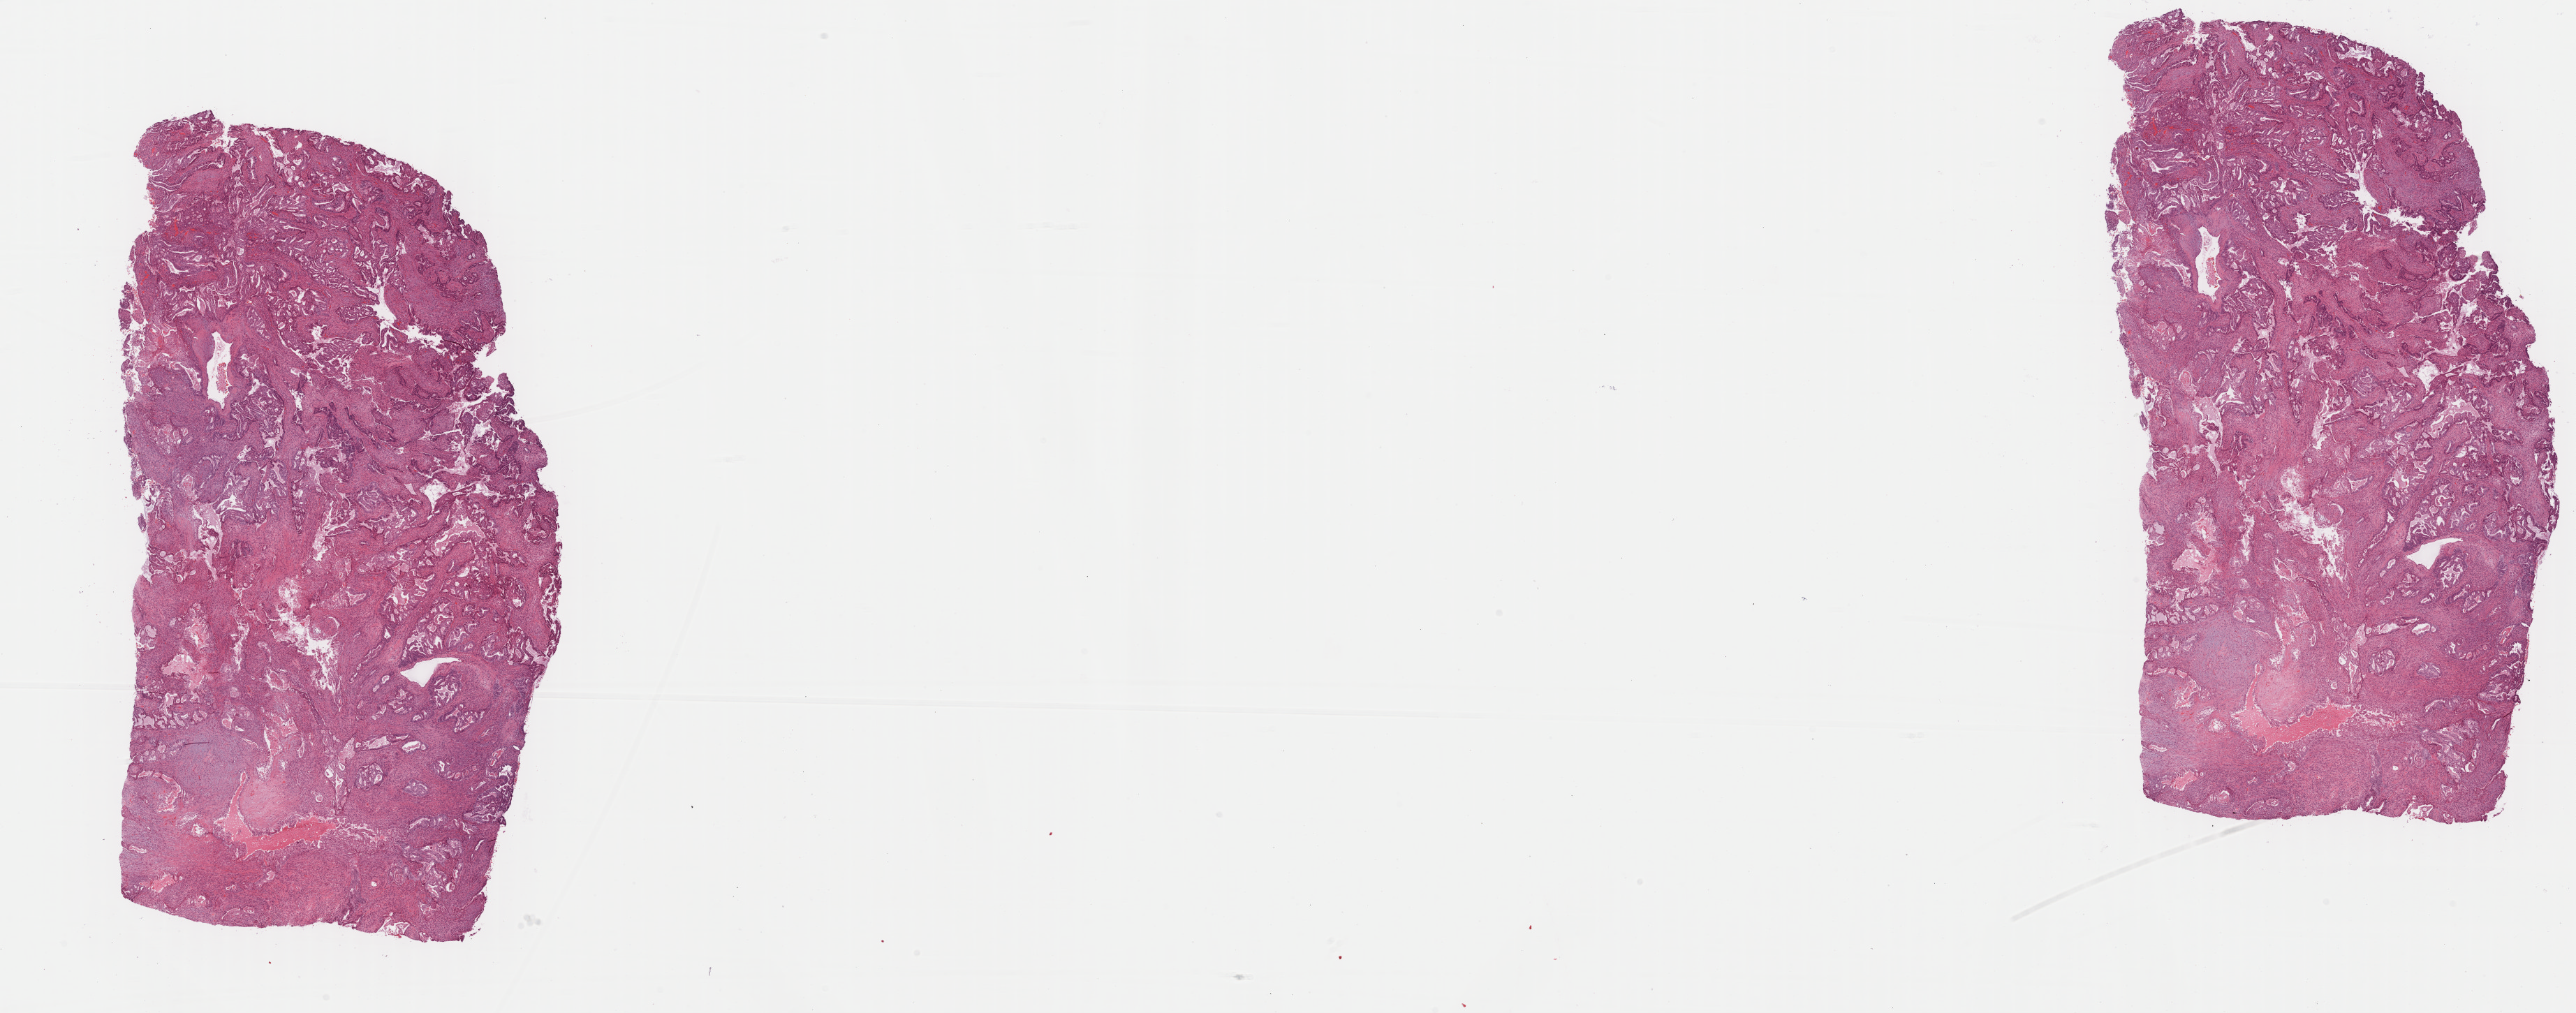
H&E-stained whole-slide image, low-resolution overview of the scanned area, about 29.1 x 11.4 mm (acquisition: 40x scan). Formalin-fixed paraffin-embedded (FFPE) diagnostic section. Sample: primary tumour, uterus. Female patient; age at initial diagnosis 60 years. Histologic grade: G2 (moderately differentiated).
• FIGO stage: IIIC
• pathologic diagnosis: Endometrioid adenocarcinoma, NOS (endometrium)
• lymph nodes positive (case pathology): 2 of 8 examined